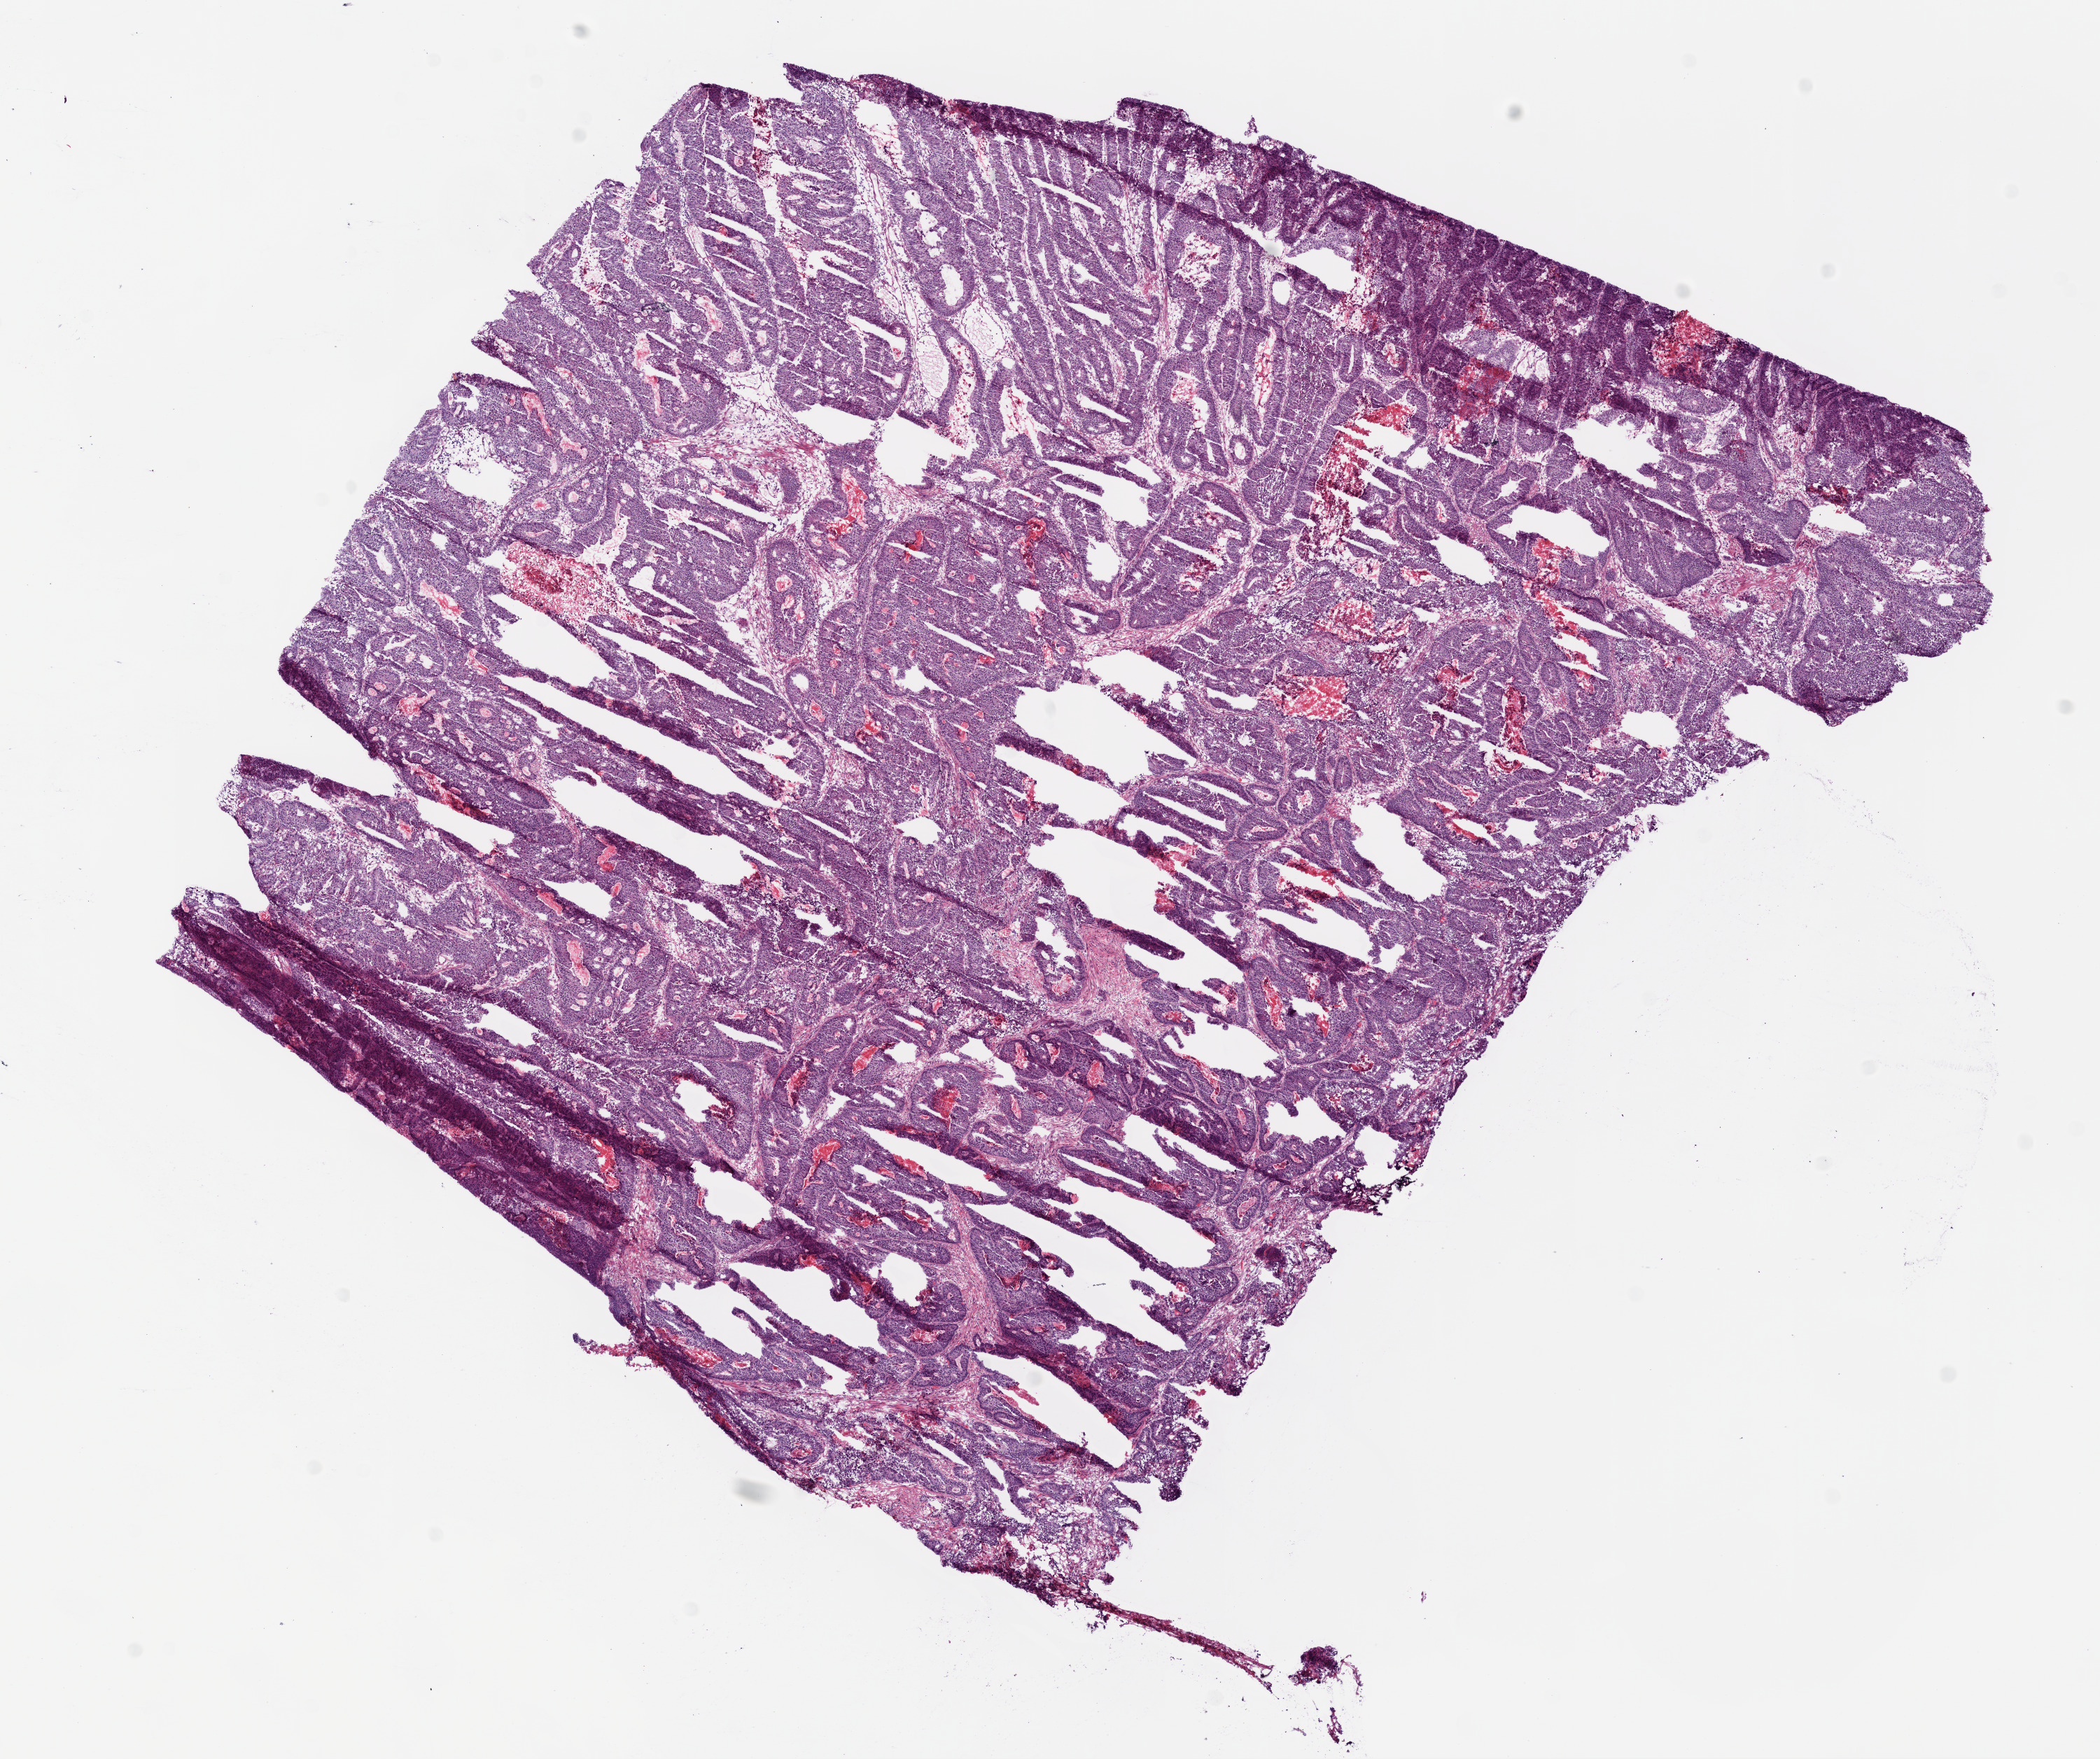
Whole-slide histology image, Hematoxylin and eosin (H&E) stained, a low-resolution overview of the entire scanned area, about 12.0 x 10.1 mm, frozen section from the bottom of the tissue portion, primary tumour sample from the colon. Male patient; age at initial diagnosis 72 years. Composition of this section per pathologist review: tumour cells 90%, tumour nuclei 90%, normal cells 0%, stromal cells 10%, necrosis 0%.
• AJCC pathologic stage: IIA (6th edition)
• diagnosis: Adenocarcinoma, NOS